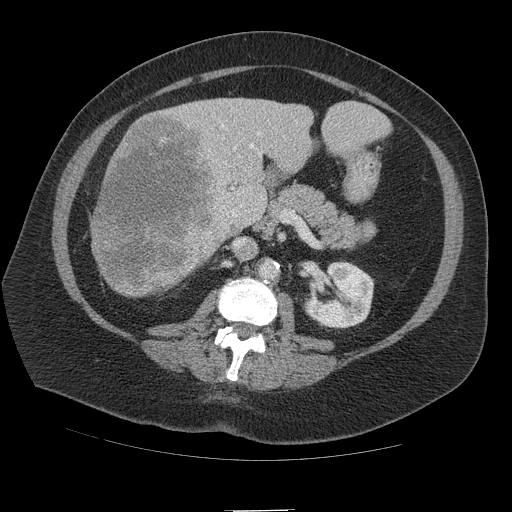
Contrast-enhanced abdominal CT (liver protocol), one axial slice. Slice 45 of 109 in the series (ordered by position). Reconstruction kernel STANDARD. 140 kVp. Soft-tissue window (W 400 / L 40 HU). 2.5 mm slice thickness. 512 × 512 image matrix, field of view 420 × 420 mm. From the clinical record (not read from this slice): diagnosis: hepatocellular carcinoma (patient treated with transarterial chemoembolisation; whether this scan precedes or follows treatment is not stated here); TNM stage (as recorded): Stage-IVB.
Annotated regions visible in this slice (semi-automatic segmentation, software-assisted and operator-edited):
- liver parenchyma outside the tumour (the mass and vessels are separate outlines, so this box may not span the whole liver): box from (x=92, y=98) to (x=367, y=296) px
- mass: (x=90, y=111)–(x=230, y=300)
- liver vessels: (x=209, y=124)–(x=261, y=217)